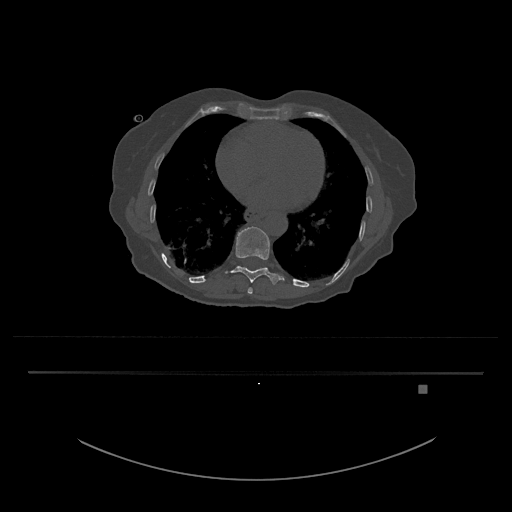
CT including the spine, one axial slice. Slice 711 of 797 in the series (ordered by position). Reconstruction kernel Br40s/3. 120 kVp. Bone window (W 1800 / L 400 HU). 0.5 mm slice thickness. 512 × 512 image matrix. Patient: female, 57 years. From the clinical record (not read from this slice): primary cancer: cervical.
Outlined on this slice (semi-automatically segmented with operator editing):
- T10 vertebra: box from (x=231, y=226) to (x=284, y=284) px
- T9 vertebra: (x=247, y=288)–(x=253, y=294)